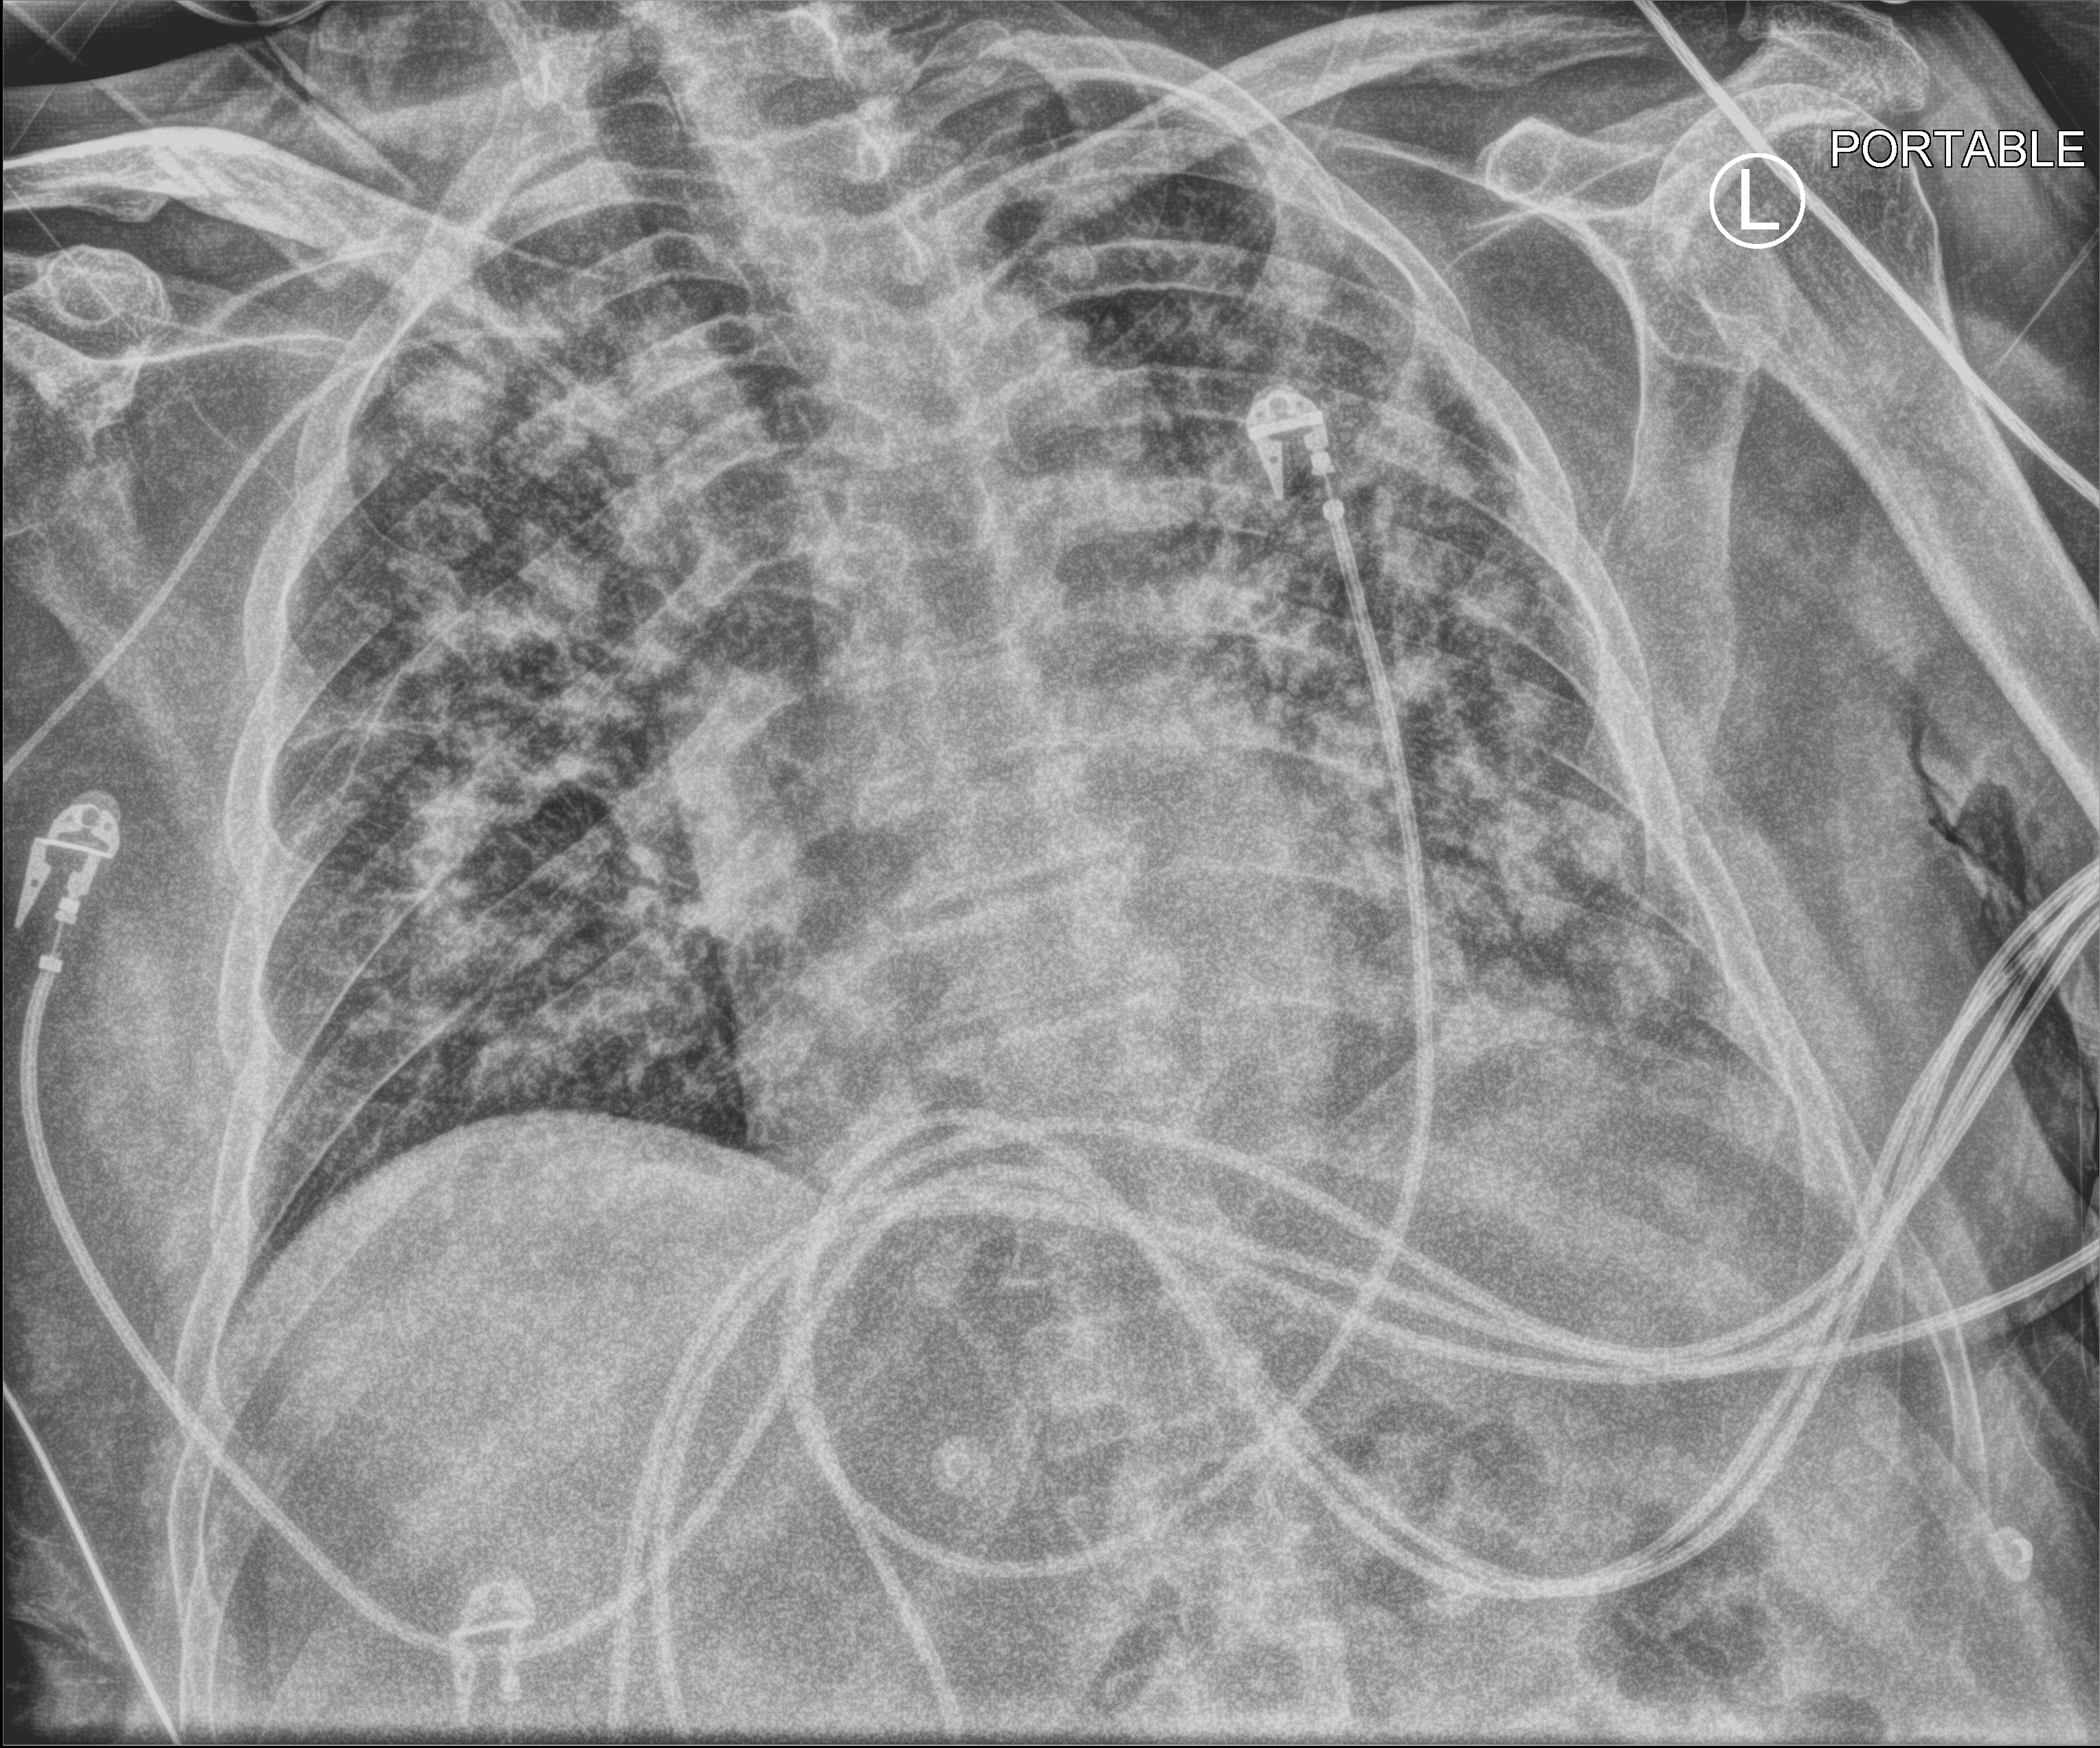
Portable chest radiograph; anteroposterior (AP) projection. Male patient hospitalised with COVID-19, age 60–74 years.
From the hospital-stay record, not from the radiograph (when in the stay this image was taken is not recorded):
- mechanically ventilated during this hospital stay: yes
- admitted to intensive care during this hospital stay: yes